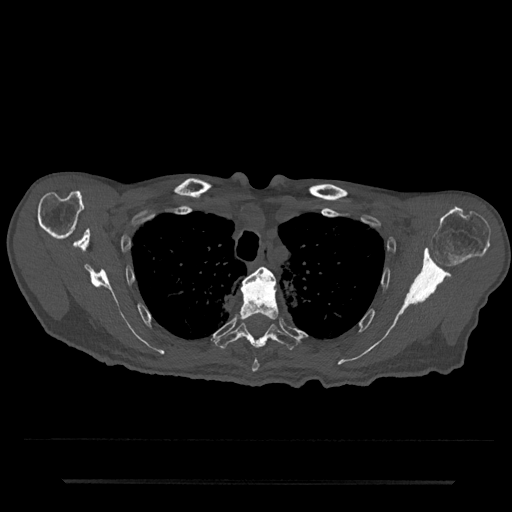
CT including the spine, one axial slice. Slice 605 of 797 in the series (ordered by position). Reconstruction kernel Br40s/3. Bone window (W 1800 / L 400 HU). 512 × 512 image matrix, field of view 427 × 427 mm. Patient: male, 74 years. Case-level facts recorded for this patient, not image findings: primary cancer: prostate.
Annotated regions visible in this slice (semi-automatic segmentation, software-assisted and operator-edited):
- T3 vertebra: bounding box <245,267,275,281> (left, top, right, bottom; pixels)
- T4 vertebra: <239,274,279,372>
- T5 vertebra: <214,322,299,351>